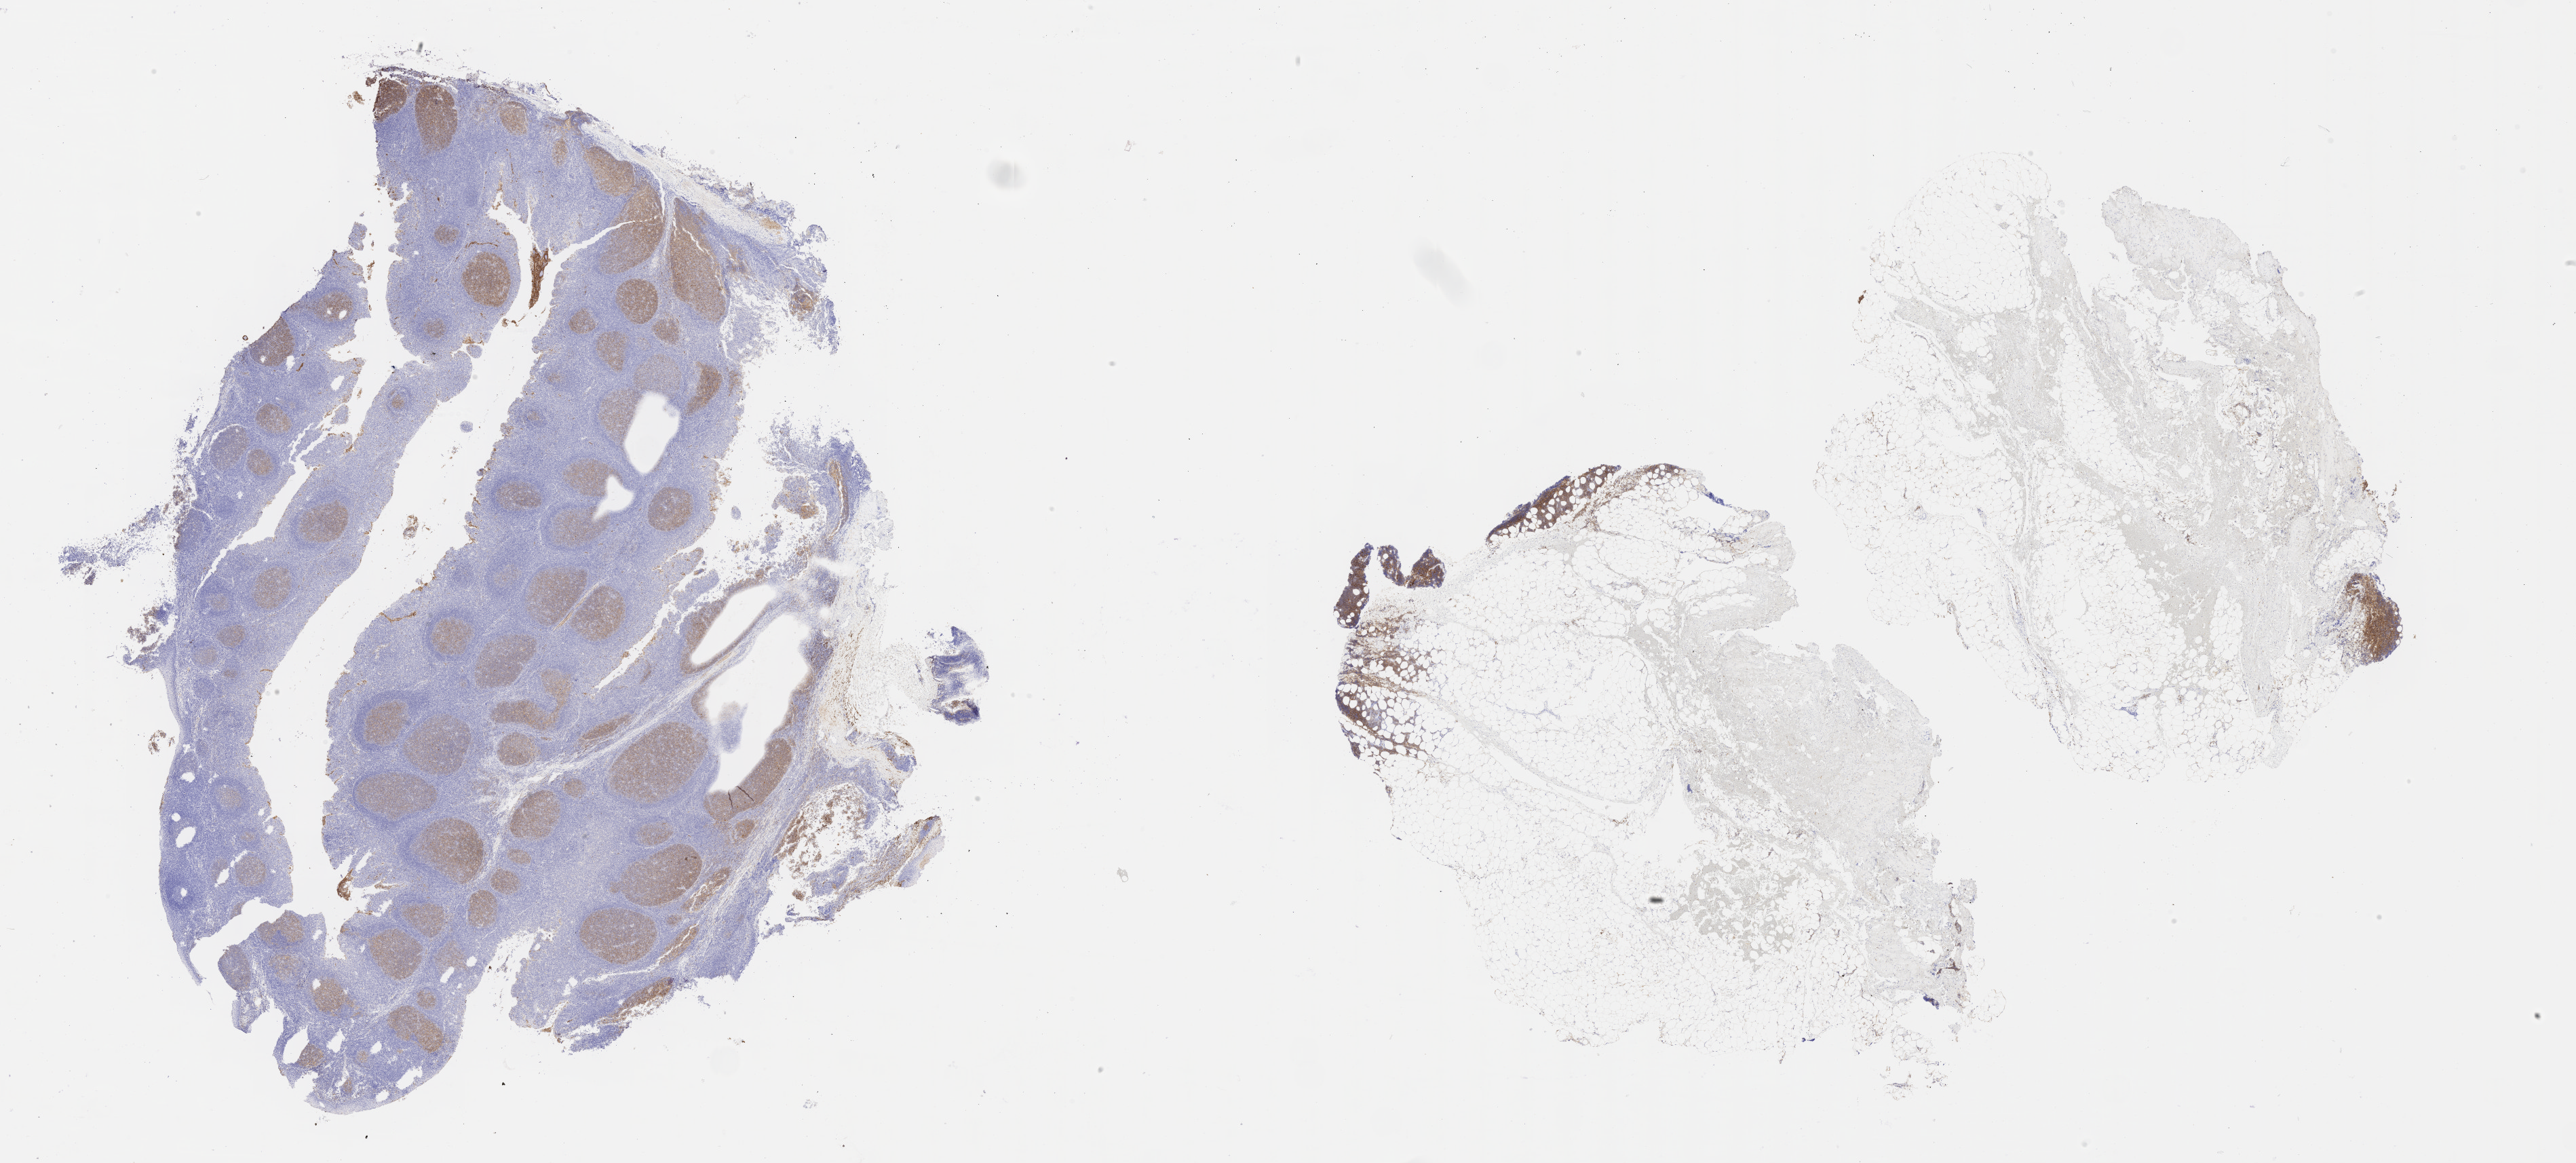
Whole-slide image, immunohistochemical stain for CD10, shown as a low-resolution overview of the whole scanned area (about 30.7 x 13.9 mm). Tumor tissue. Anatomic site: upper limb lymph node. Patient male; age 76 years.
Diagnosis: Burkitt lymphoma, NOS.